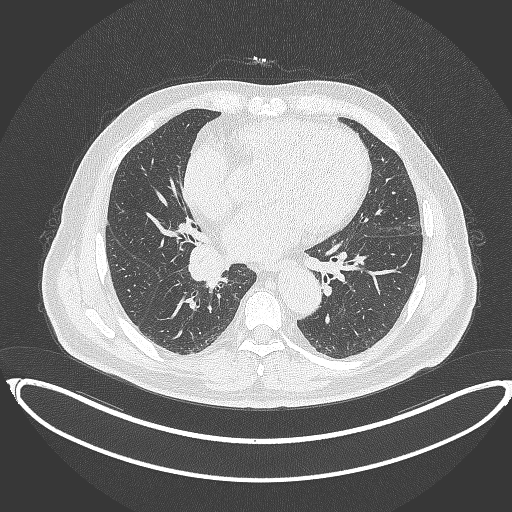
Chest CT, one axial slice. Slice 186 of 387 in the series (ordered by position). 120 kVp. Lung window (W 1500 / L -600 HU). 512 × 512 image matrix. Patient: male, 61 years. Case-level facts recorded for this patient, not image findings: clinical TNM (as recorded): T1b N1 M0.
Annotated regions visible in this slice (rectangle marked by the reading radiologist):
- lung tumour (recorded histology: squamous cell carcinoma): bounding box <185,238,228,288> (left, top, right, bottom; pixels)